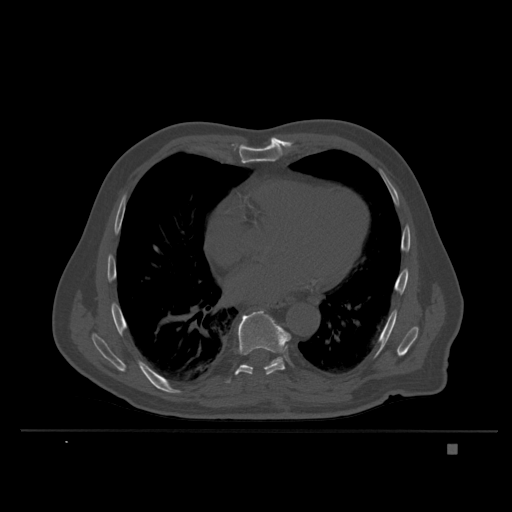
CT including the spine, one axial slice; slice 227 of 435 in the series (ordered by position); bone window (W 1800 / L 400 HU); 1.5 mm slice thickness; 512 × 512 image matrix, field of view 434 × 434 mm. Male patient, age 73 years. From the clinical record (not read from this slice): primary cancer: skin.
Annotated regions visible in this slice (semi-automatic segmentation, software-assisted and operator-edited):
- T8 vertebra: bounding box <225,309,291,384> (left, top, right, bottom; pixels)
- T9 vertebra: <268,357,282,366>